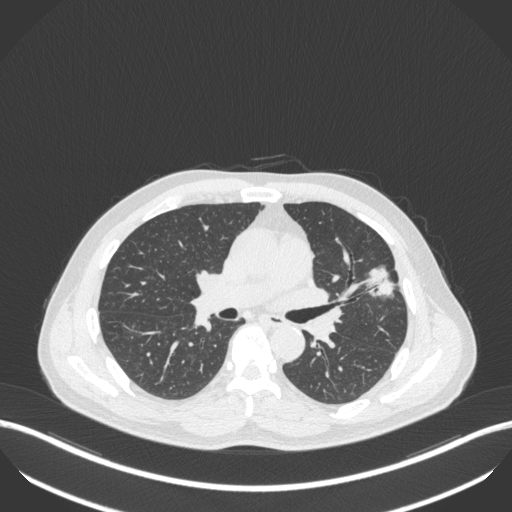
Chest CT, one axial slice. Slice 226 of 418 in the series (ordered by position). Reconstruction kernel B31f. 120 kVp. Lung window (W 1500 / L -600 HU). 1 mm slice thickness. 512 × 512 image matrix. Patient: male, 55 years. From the clinical record (not read from this slice): clinical TNM (as recorded): T1c N0 M0.
Structures marked on this image (bounding box drawn by a radiologist):
- lung tumour (recorded histology: adenocarcinoma): bounding box (x1, y1, x2, y2) in pixels: (363, 265, 397, 301)